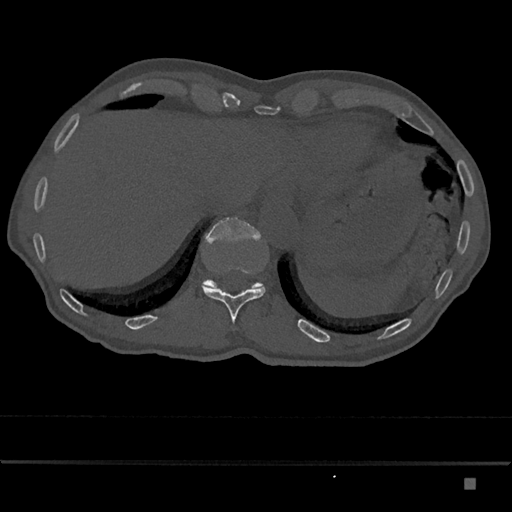
CT including the spine, one axial slice; slice 661 of 797 in the series (ordered by position); reconstruction kernel Br40s/3; 120 kVp; bone window (W 1800 / L 400 HU); 0.5 mm slice thickness; 512 × 512 image matrix, field of view 390 × 390 mm. Patient: male, 72 years. Case-level facts recorded for this patient, not image findings: primary cancer: prostate.
Outlined on this slice (semi-automatic segmentation, software-assisted and operator-edited):
- T11 vertebra: bounding box [x1, y1, x2, y2] px = [201, 266, 266, 324]
- T12 vertebra: [203, 217, 263, 289]